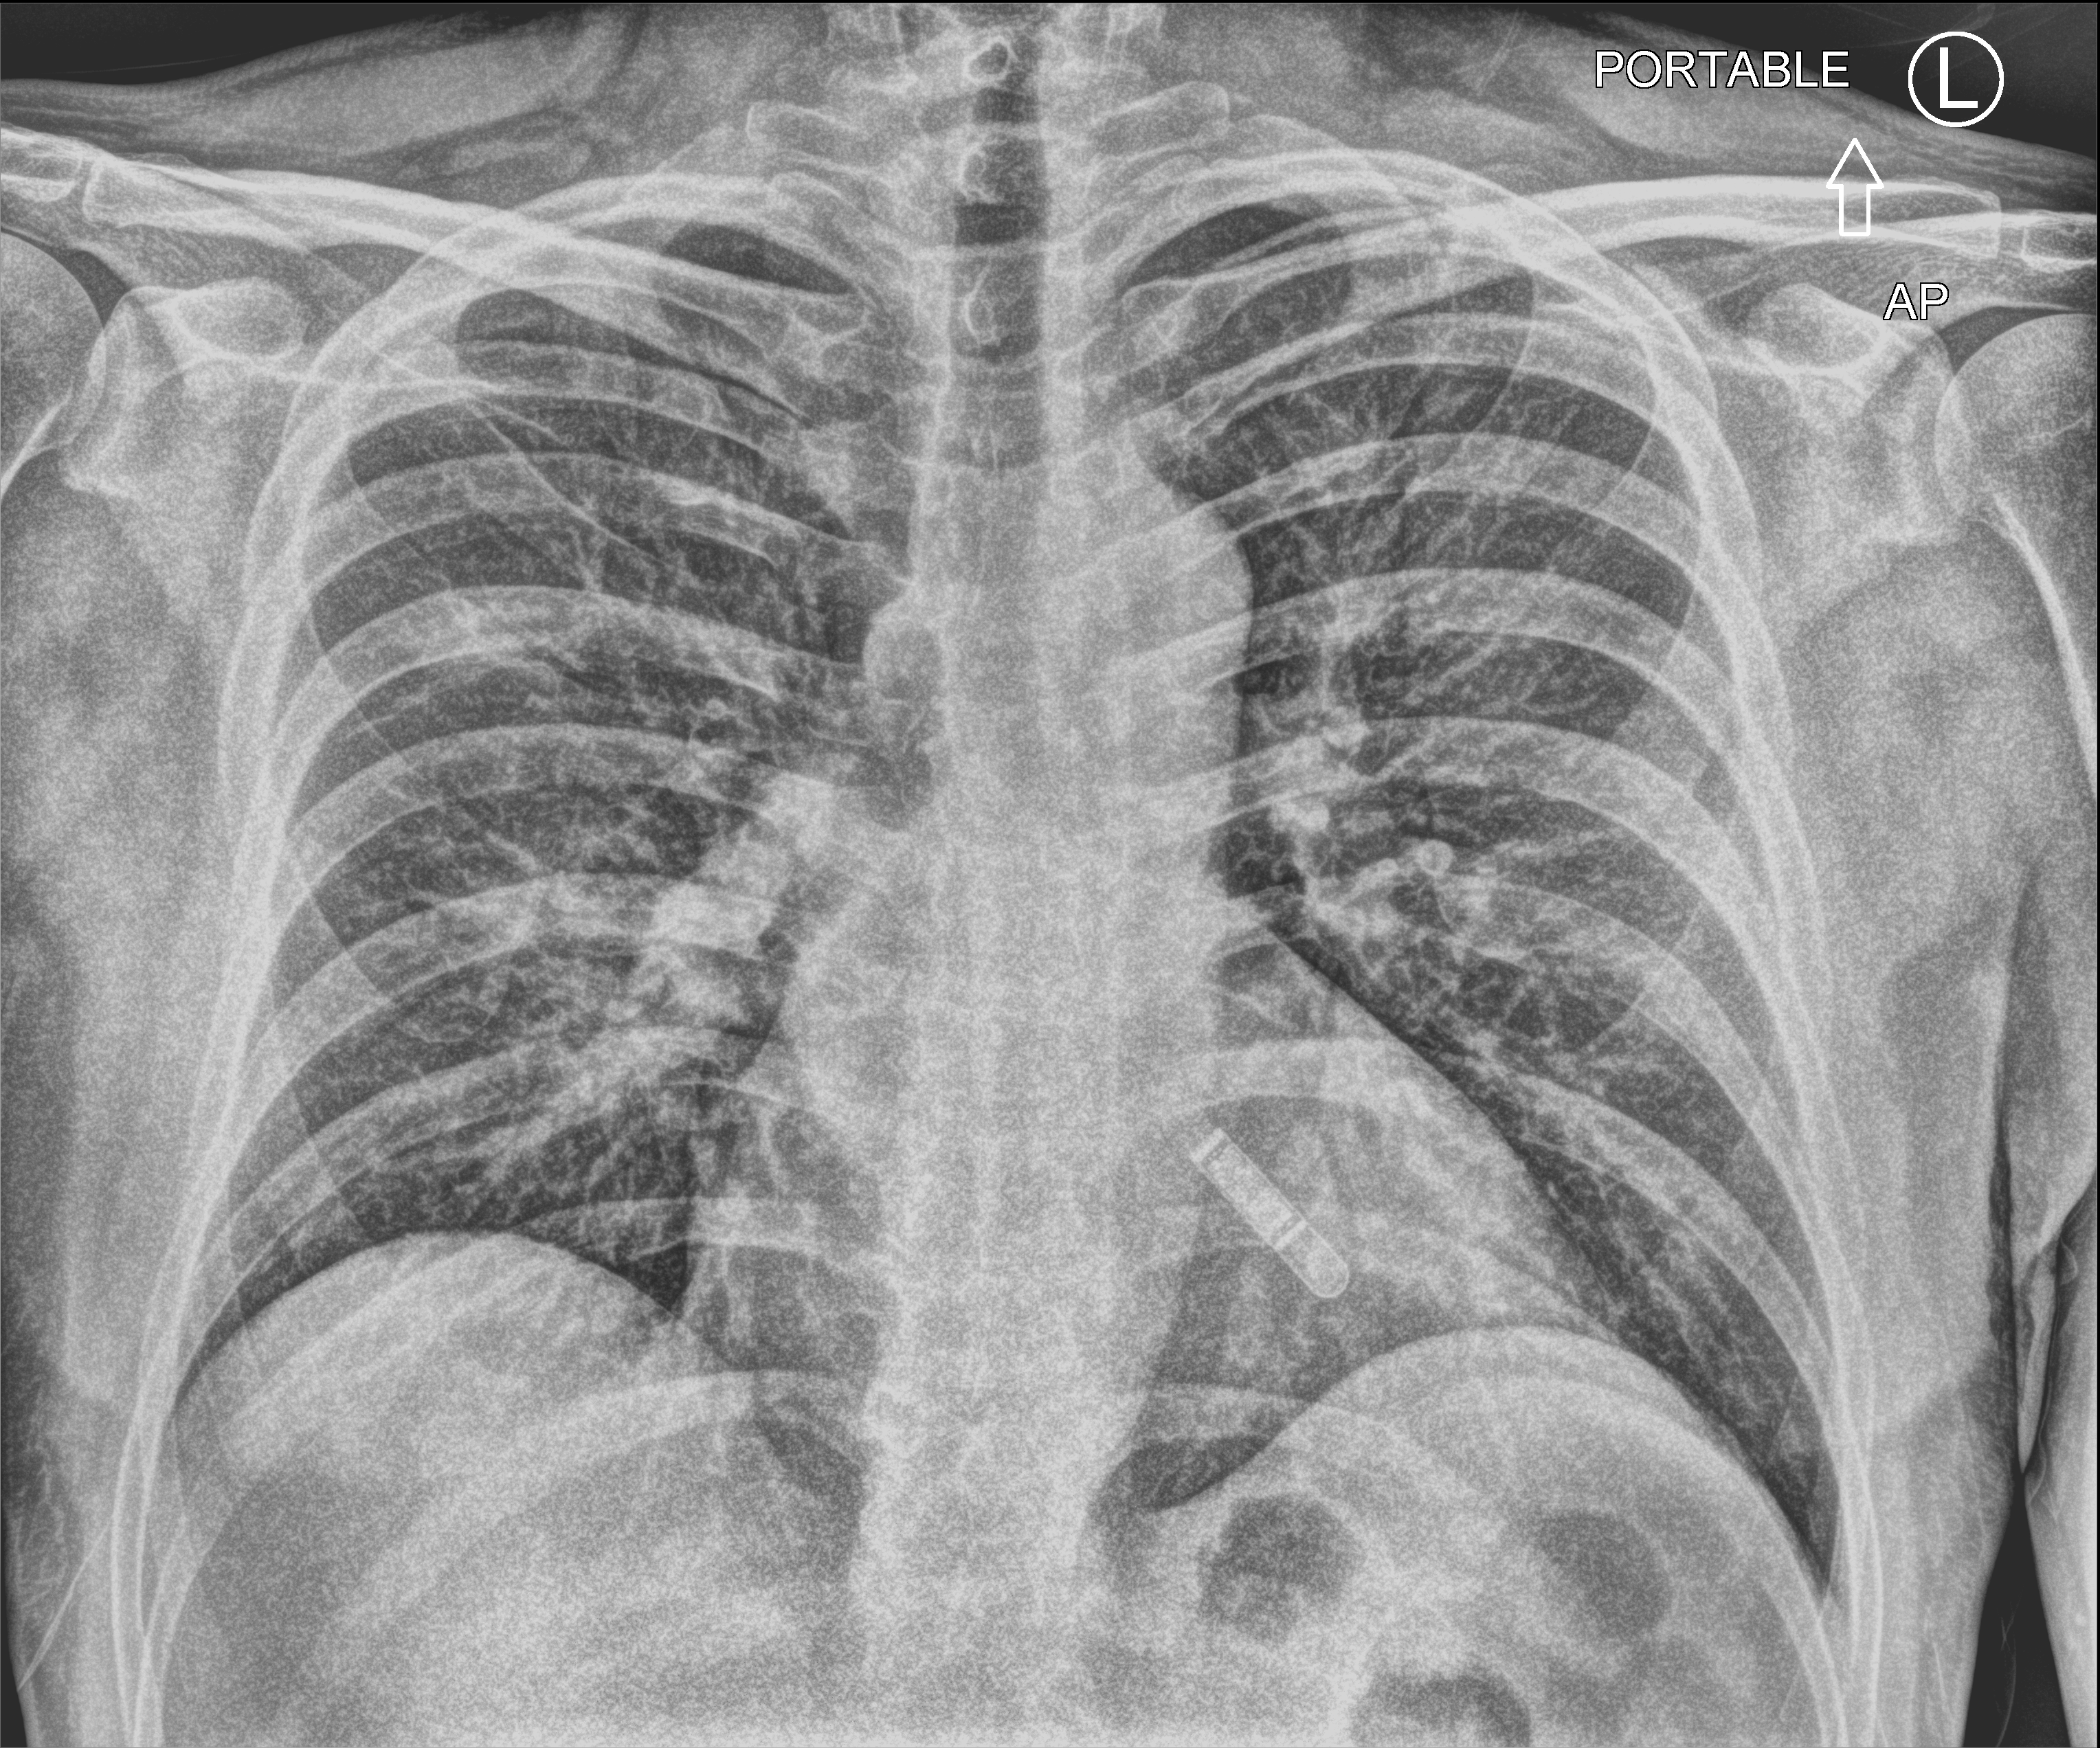
Bedside chest radiograph (computed radiography), anteroposterior (AP) projection. Male patient hospitalised with COVID-19, age 18–59 years.
Hospital-stay facts (about this admission, not read from this image; timing relative to this image not recorded): admitted to intensive care during this hospital stay: no.